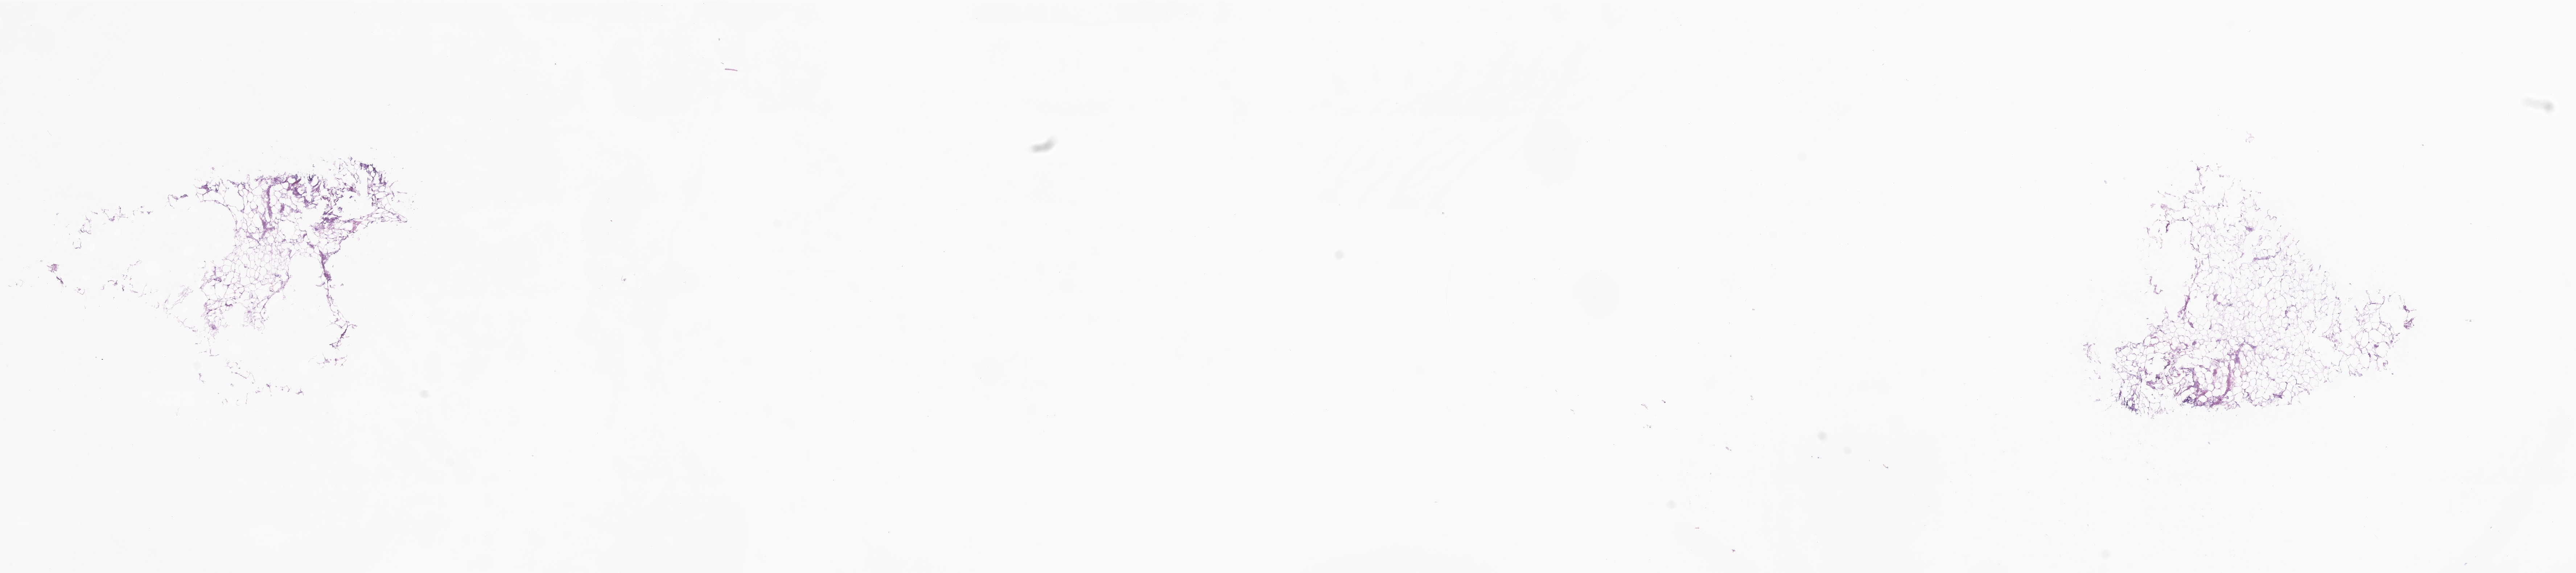
Whole-slide image, H&E stain, a low-resolution overview of the entire scanned area, about 29.9 x 6.7 mm; frozen section; primary tumor; site: breast. Female patient; age at initial diagnosis 66 years. Composition of this section per pathologist review: tumor cells 0%, tumor nuclei 0%, stromal cells 99%, necrosis 0%, normal cells 1%. Infiltration values recorded for this section: lymphocyte infiltration 20%, monocyte infiltration 0%, neutrophil infiltration 0%.
Diagnosis: Infiltrating duct carcinoma, NOS.